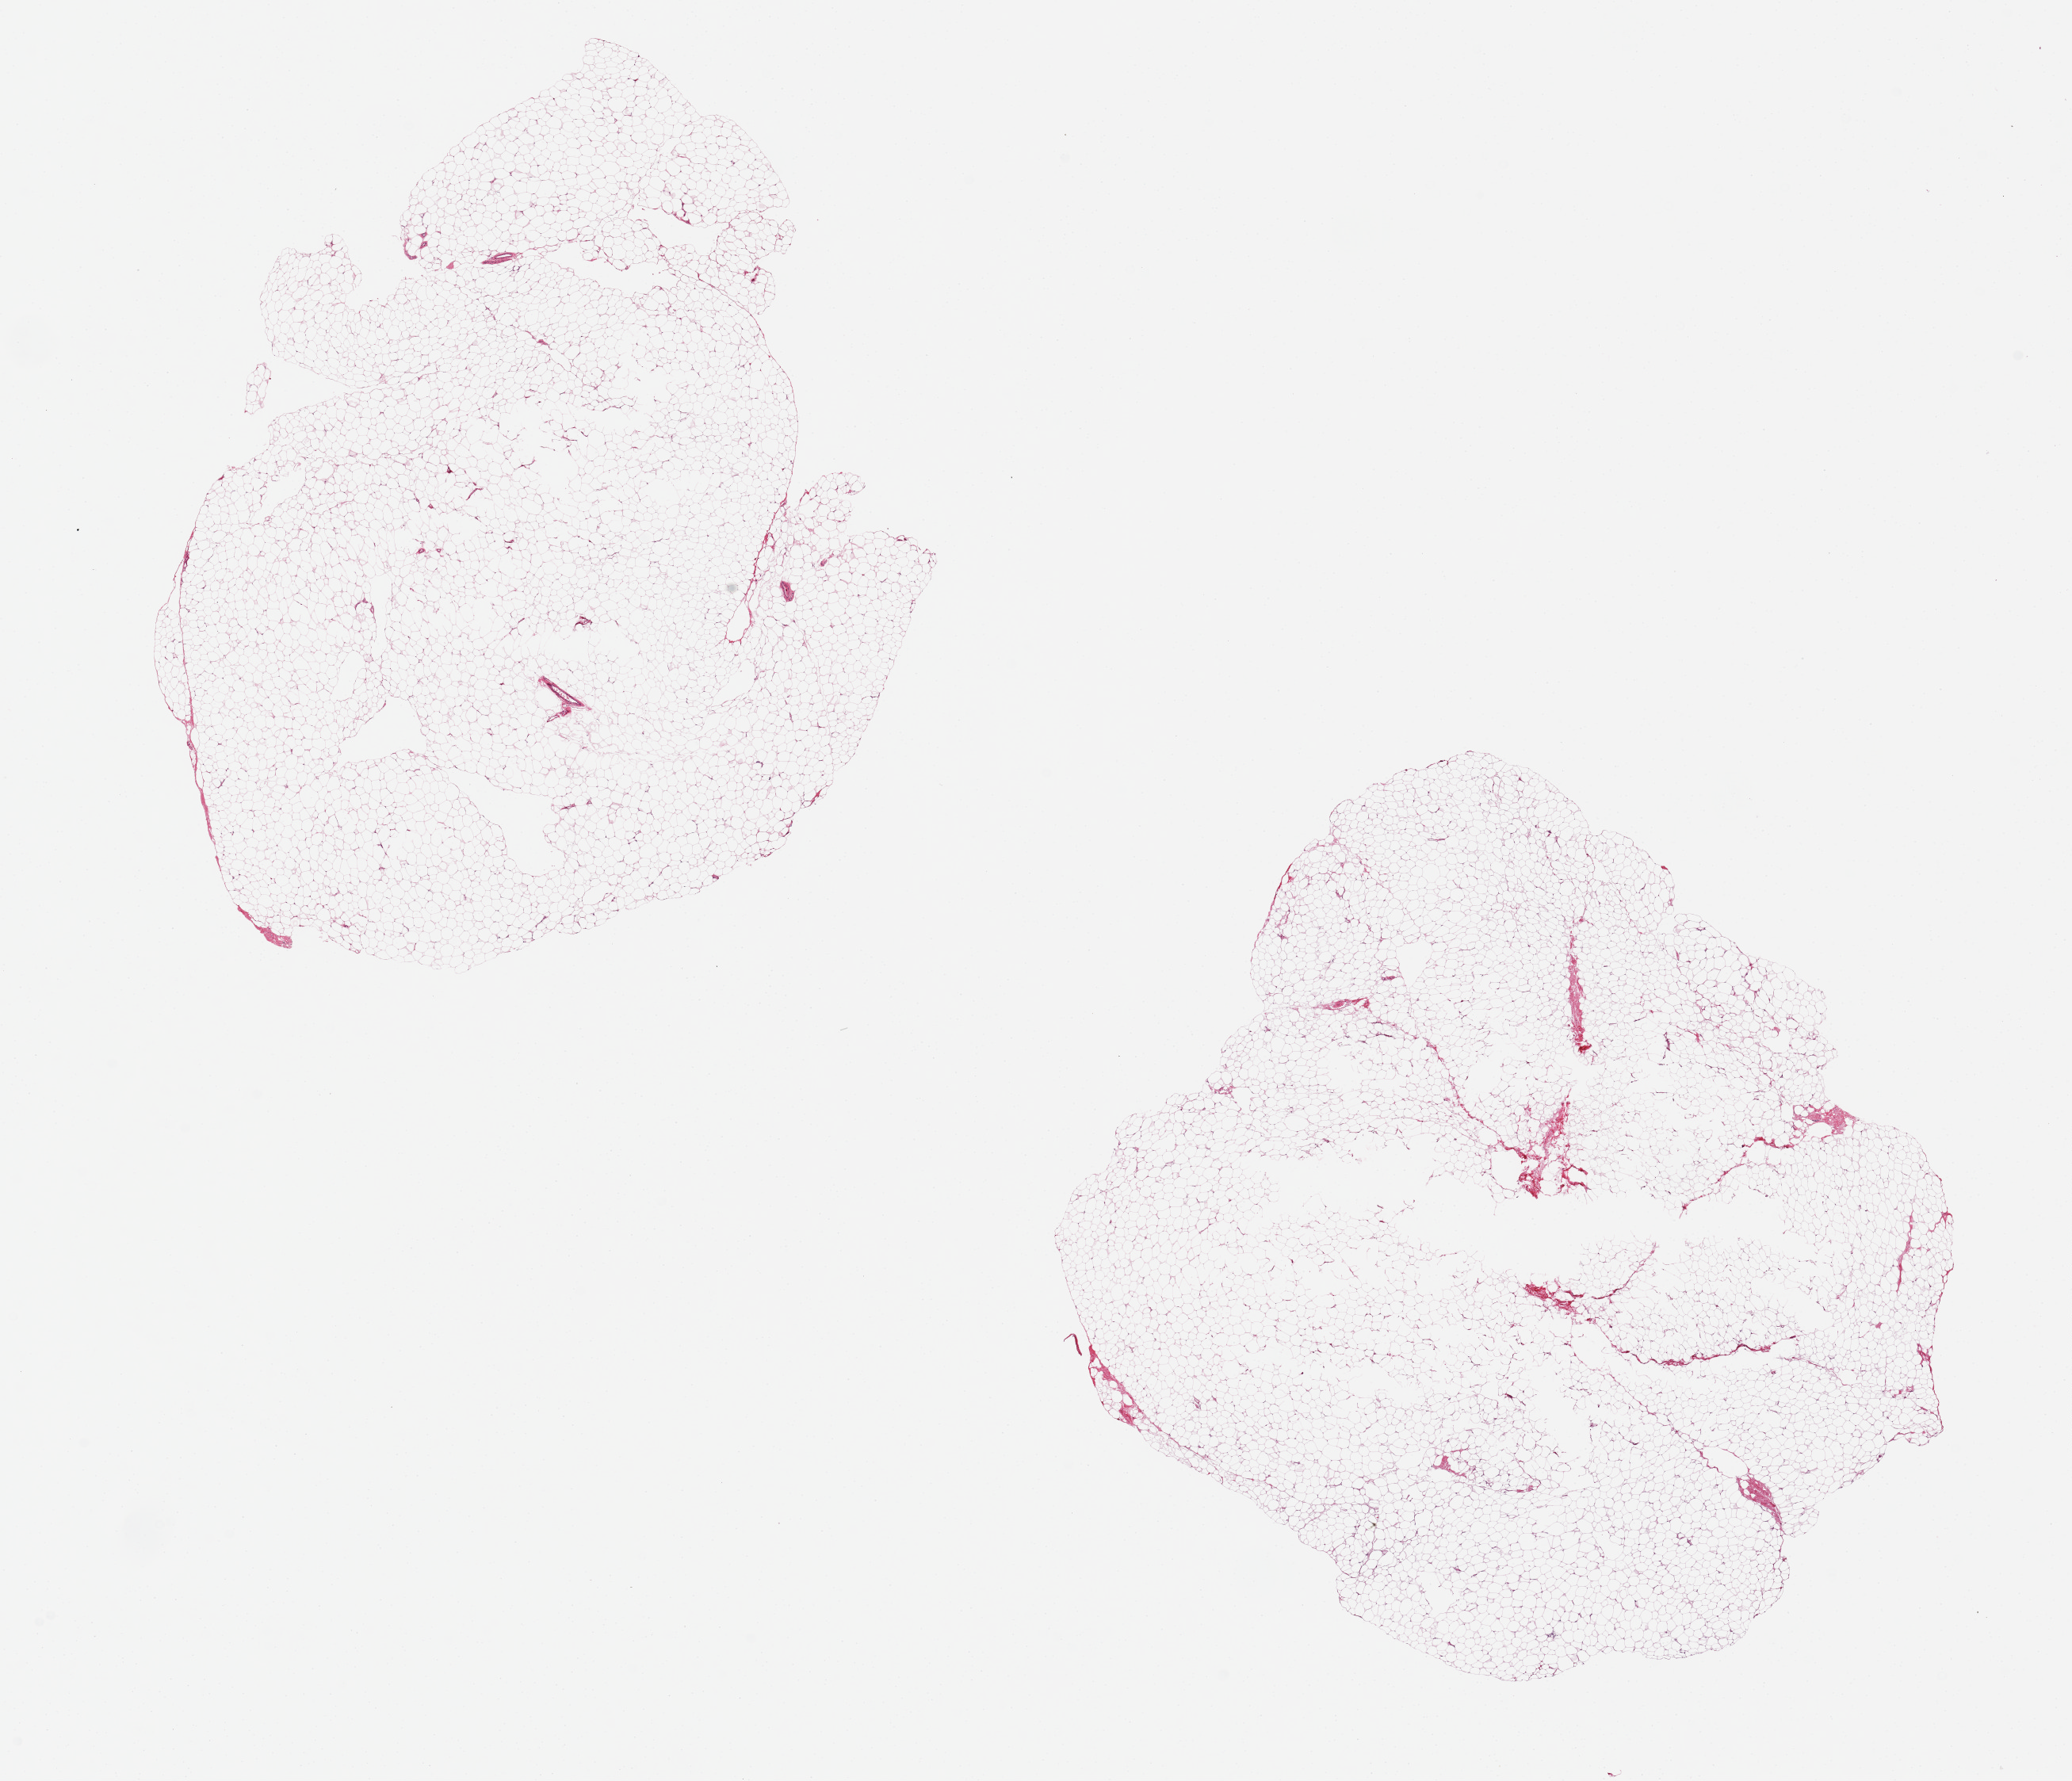
Haematoxylin and eosin whole-slide image, brightfield, whole scanned area (about 20.7 x 17.8 mm, acquisition: 20x scan) shown as a low-resolution overview. PAXgene-fixed paraffin-embedded (PFPE) section. Section of breast (target tissue). Donor tissue sample. Donor: male.
Review note (as recorded): 2 alqiuots, ~8x8mm. All adipose, no ductal elements noted.